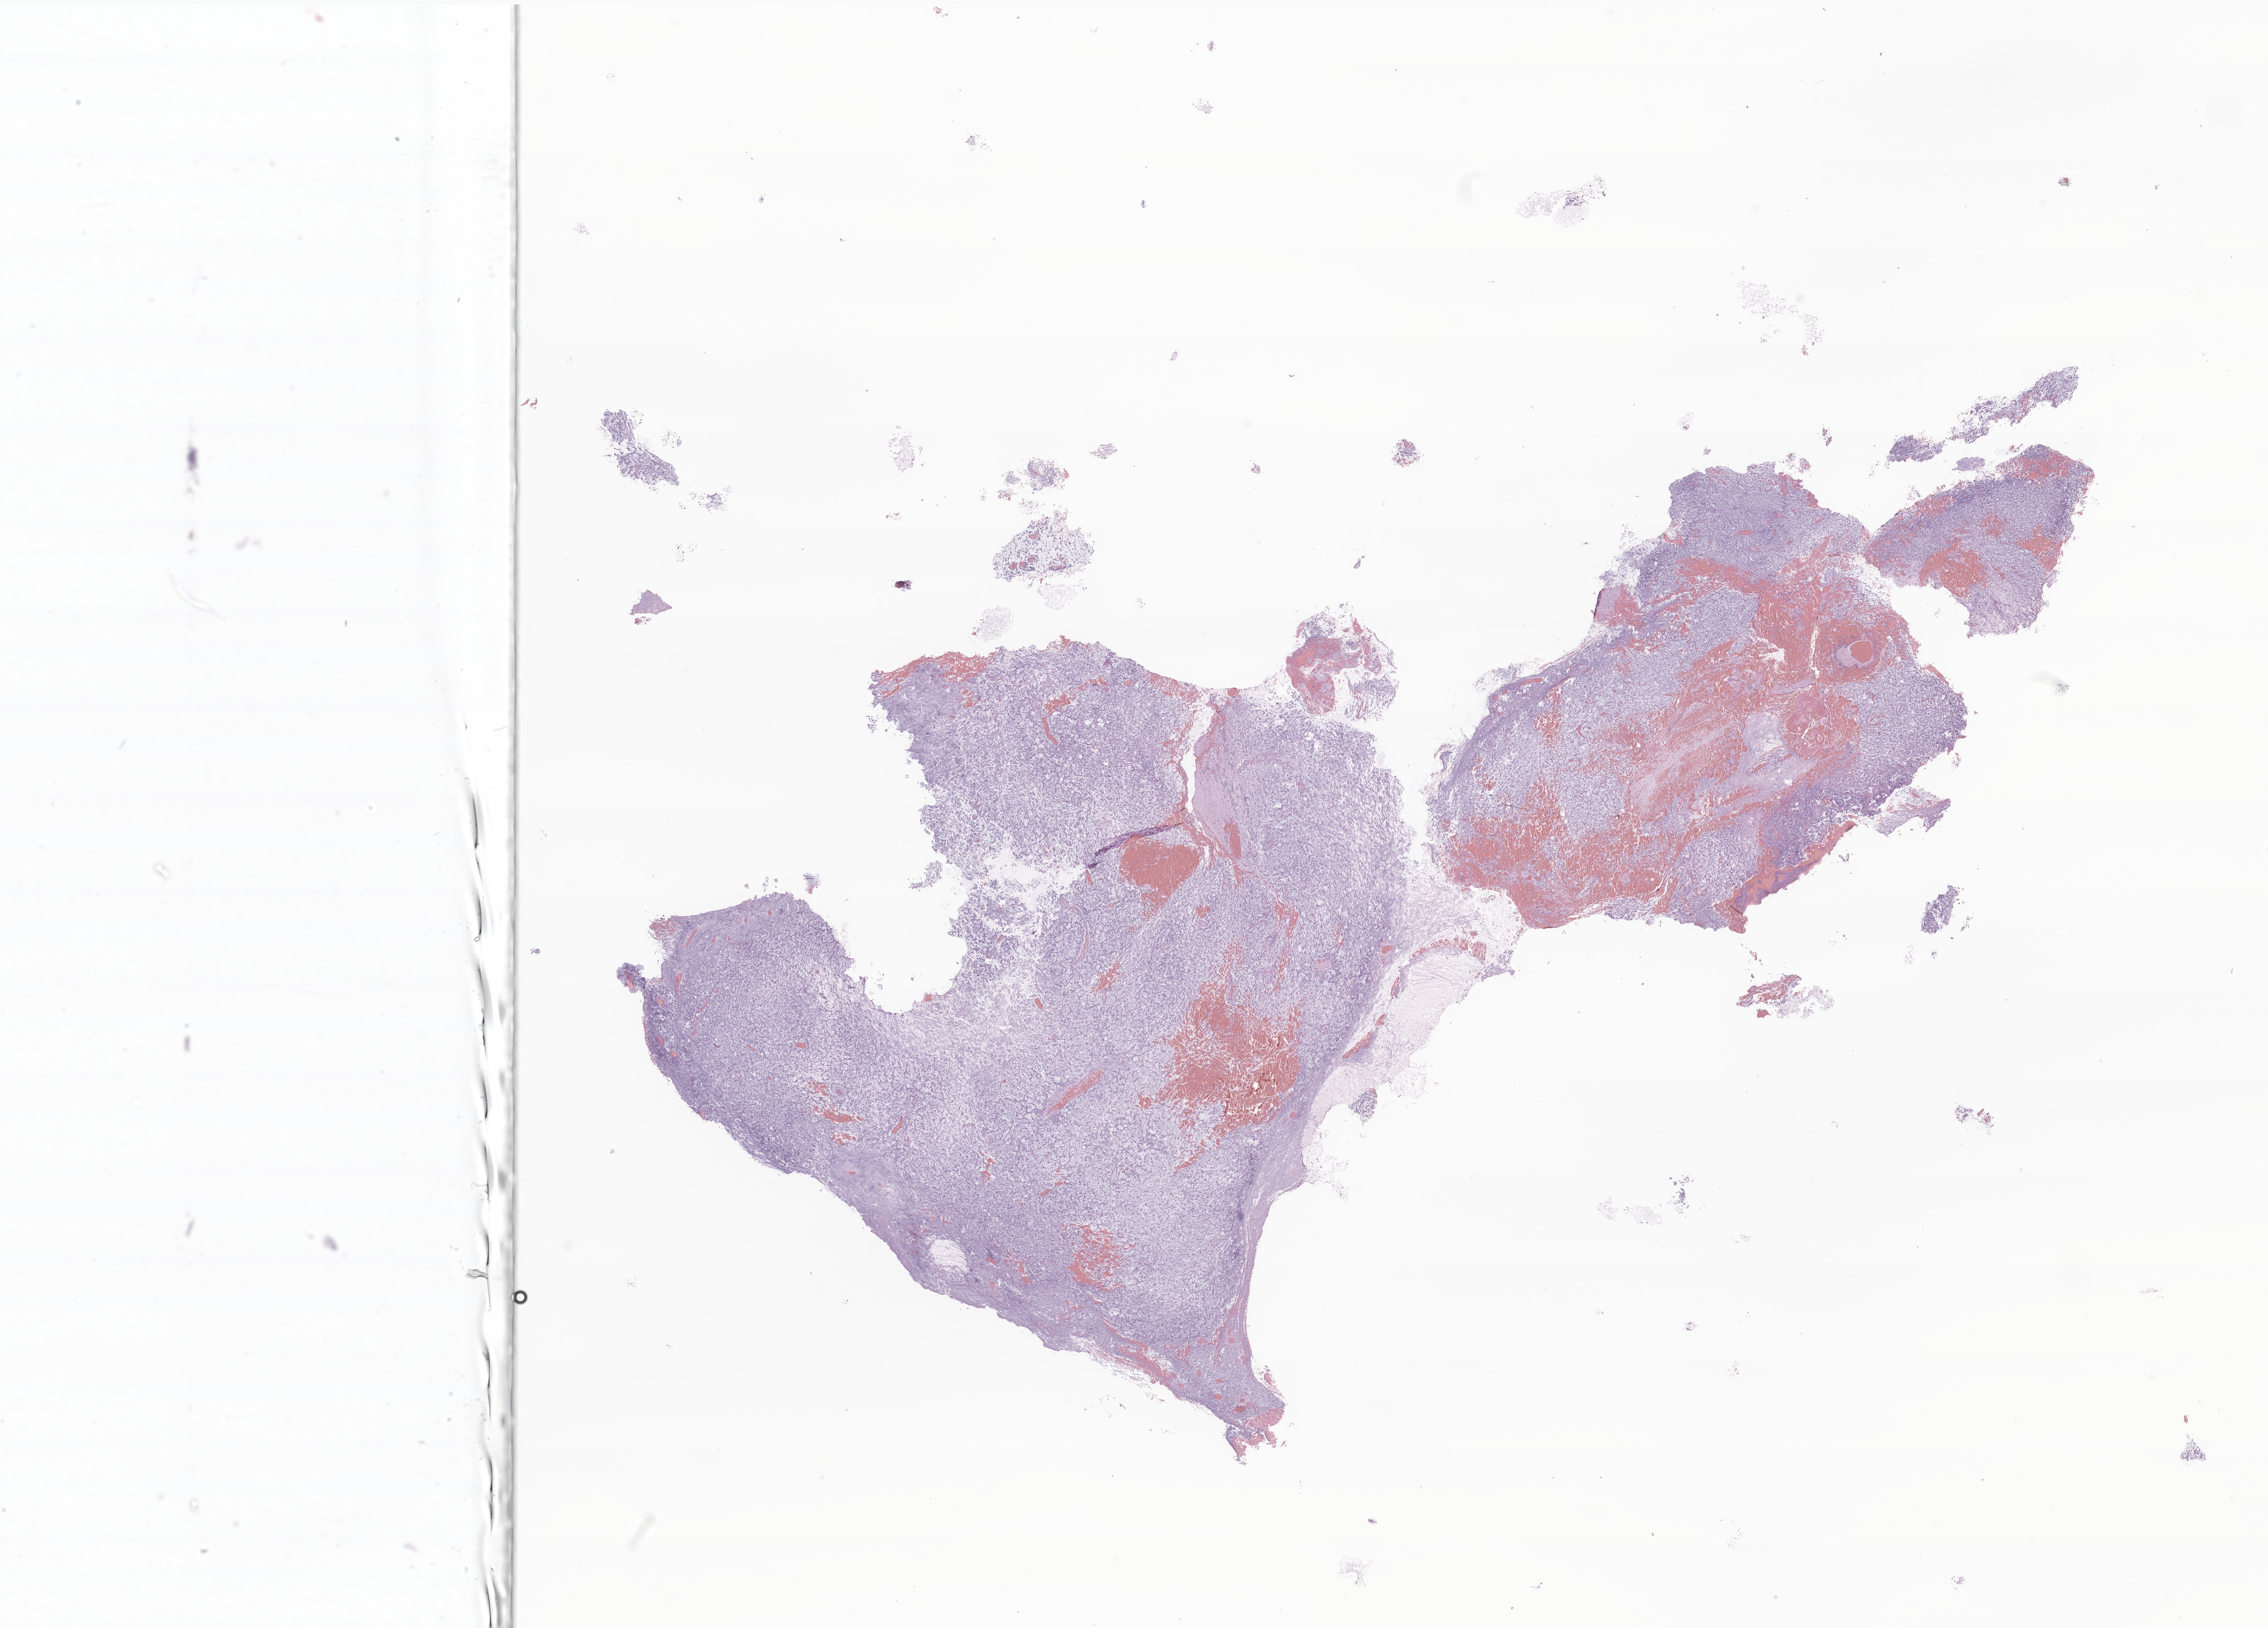
Digitized H&E-stained section of tumor tissue from the brain, whole scanned area (about 26.2 x 18.8 mm) shown as a low-resolution overview. Formalin-fixed, paraffin-embedded (FFPE) tissue. Patient: male, age 588 days (about 1.6 years).
* diagnosis: Neoplasm, malignant